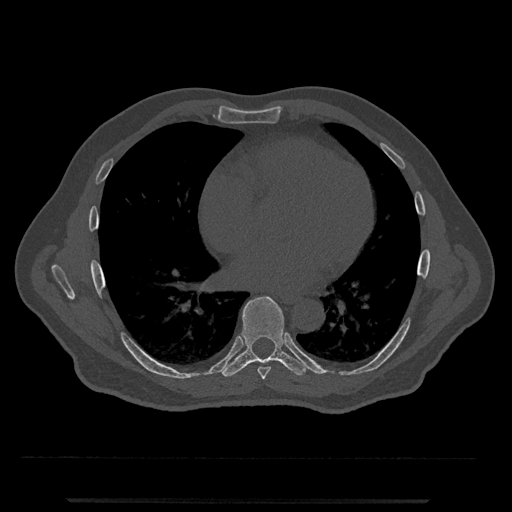
CT including the spine, one axial slice. Position 647 of 797 along the scan axis. Reconstruction kernel Br40s/3. 120 kVp. Bone window (W 1800 / L 400 HU). 0.5 mm slice thickness. 512 × 512 image matrix, field of view 419 × 419 mm. Male patient, age 63 years. From the clinical record (not read from this slice): primary cancer: prostate.
Structures marked on this image (semi-automatic segmentation, software-assisted and operator-edited):
- T7 vertebra: bounding box [x1, y1, x2, y2] px = [257, 367, 271, 380]
- T8 vertebra: [222, 296, 309, 377]